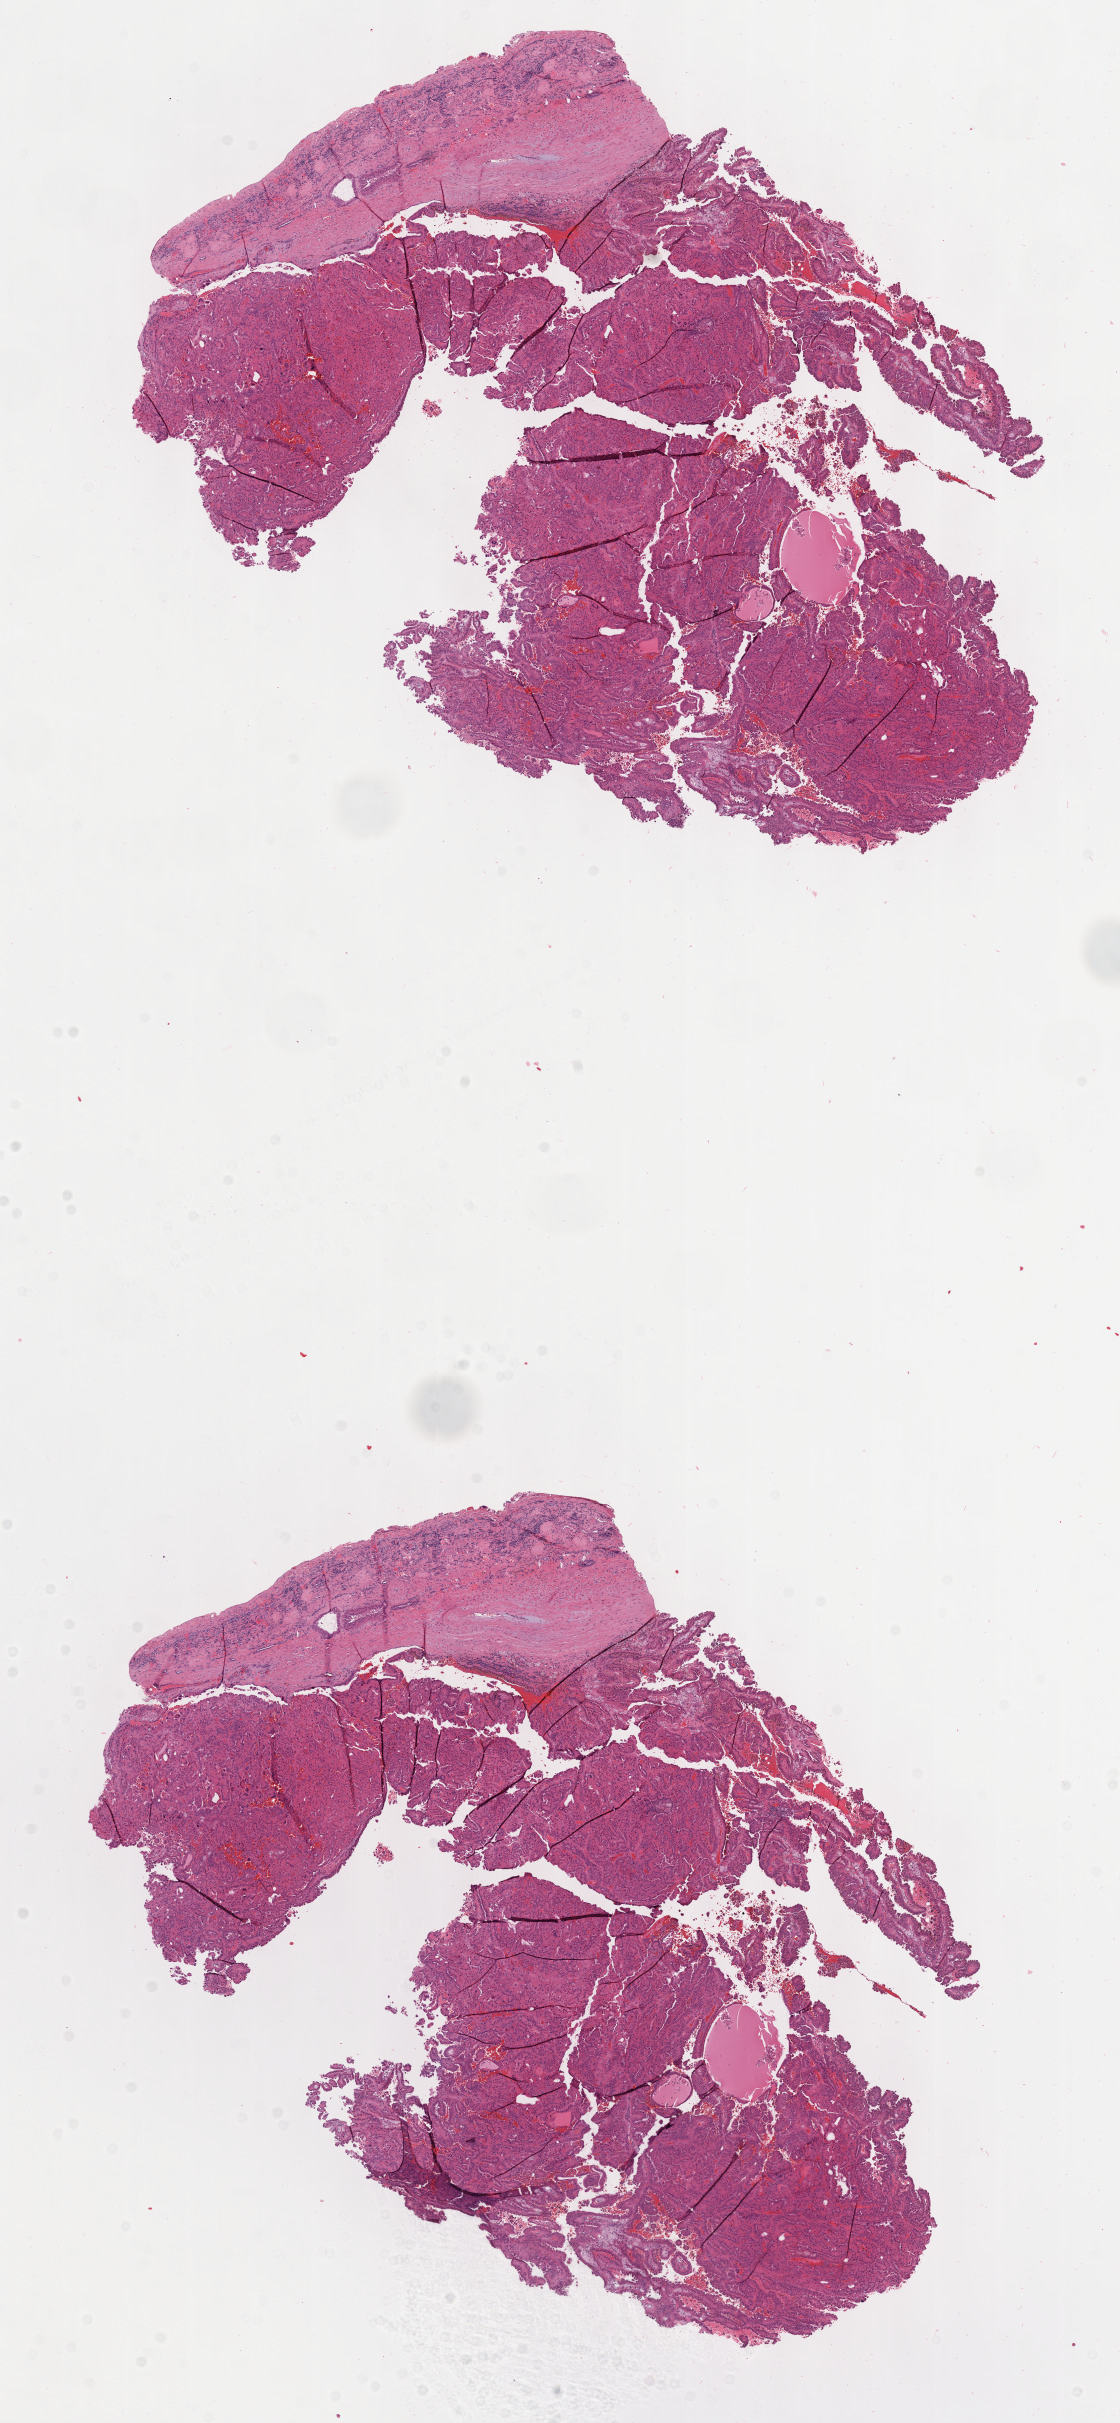
Digitized H&E-stained tissue section (whole slide) — a low-resolution overview of the entire scanned area, about 9.1 x 19.6 mm (slide scanned at 40x); FFPE section; primary tumour sample from the kidney. Male, age 74 years at initial diagnosis.
AJCC pathologic stage: I. Diagnosis: Papillary adenocarcinoma, NOS. Laterality: right.